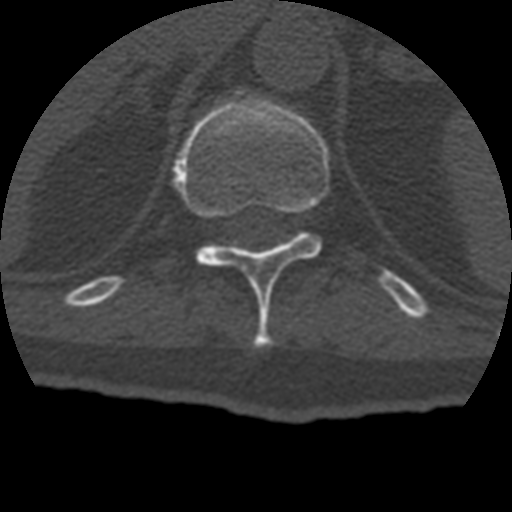
CT including the spine, one axial slice. Slice 192 of 399 in the series (ordered by position). 120 kVp. Bone window (W 1800 / L 400 HU). 1.25 mm slice thickness. 512 × 512 image matrix. Patient age 69 years. From the clinical record (not read from this slice): primary cancer: prostate.
Annotated regions visible in this slice (semi-automatically segmented with operator editing):
- T11 vertebra: bounding box <173,98,330,348> (left, top, right, bottom; pixels)